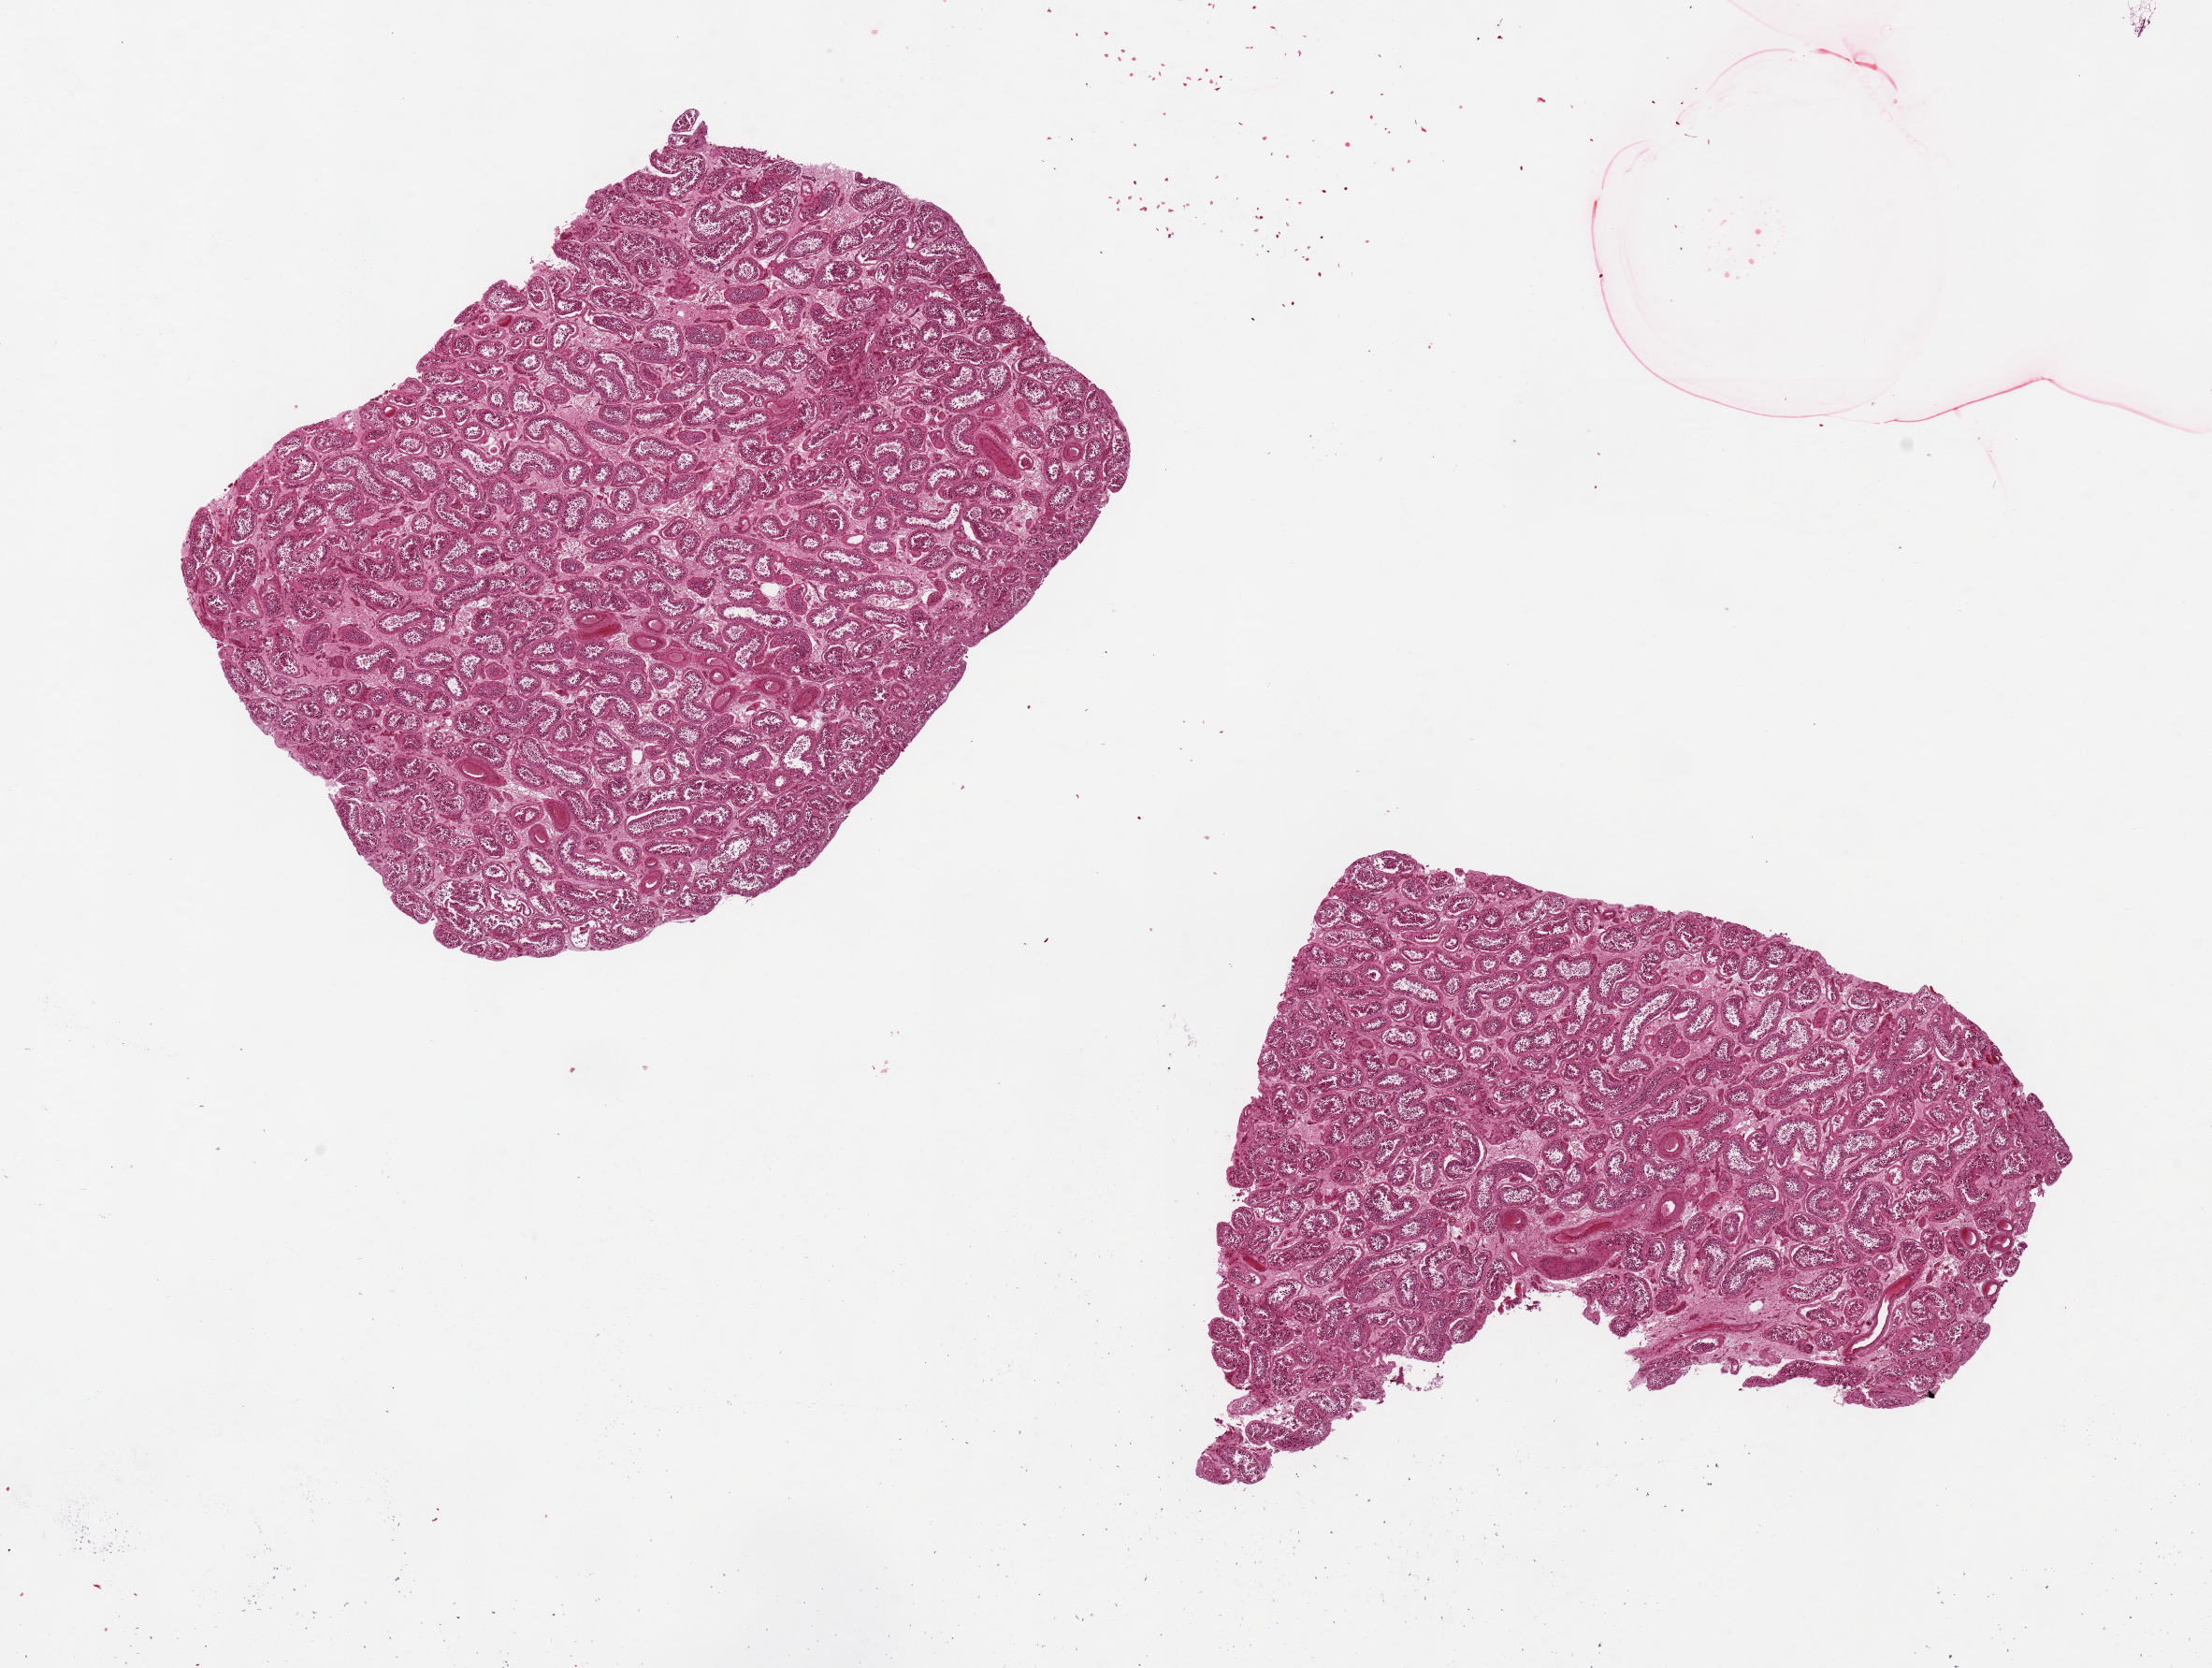
Whole-slide image, haematoxylin and eosin stain — a low-resolution overview of the entire scanned area, about 18.7 x 14.1 mm (slide scanned at 20x), PAXgene-fixed, paraffin-embedded tissue, sampled site (target tissue): testis, donor tissue sample. Male donor.
Reviewer comment on this tissue sample: 2 pieces ~7x5. Moderate -- severe autolysis.